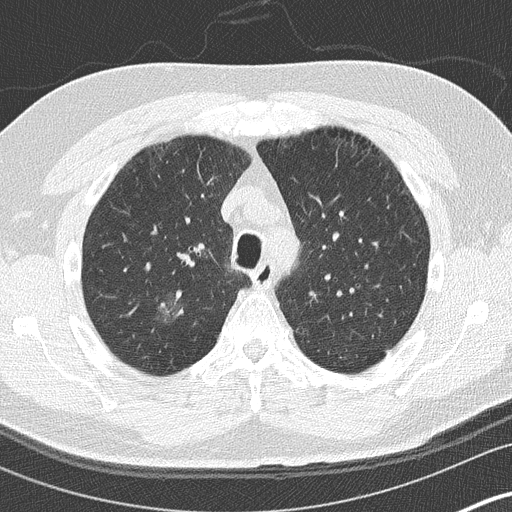
Chest CT (low-dose screening protocol), one axial image. Baseline annual screen. Lung window (W 1500 / L -600 HU). 2 mm slice thickness. 512 × 512 image matrix, field of view 310 × 310 mm. Male, age 59 years at enrolment.
• Expert-annotated lung lesion, bounding box <147,288,202,344> (left, top, right, bottom; pixels).
• Reader record for this screening exam (exam-level; its link to the box is not recorded): non-calcified nodule or mass ≥4 mm, right upper lobe, 16 × 16 mm, ground glass attenuation.
• Later outcome: lung cancer diagnosed 456 days after this screen (after the second annual screen) — bronchiolo-alveolar adenocarcinoma, NOS, right lower lobe, stage IA (AJCC 6th edition), 15 mm at pathology.